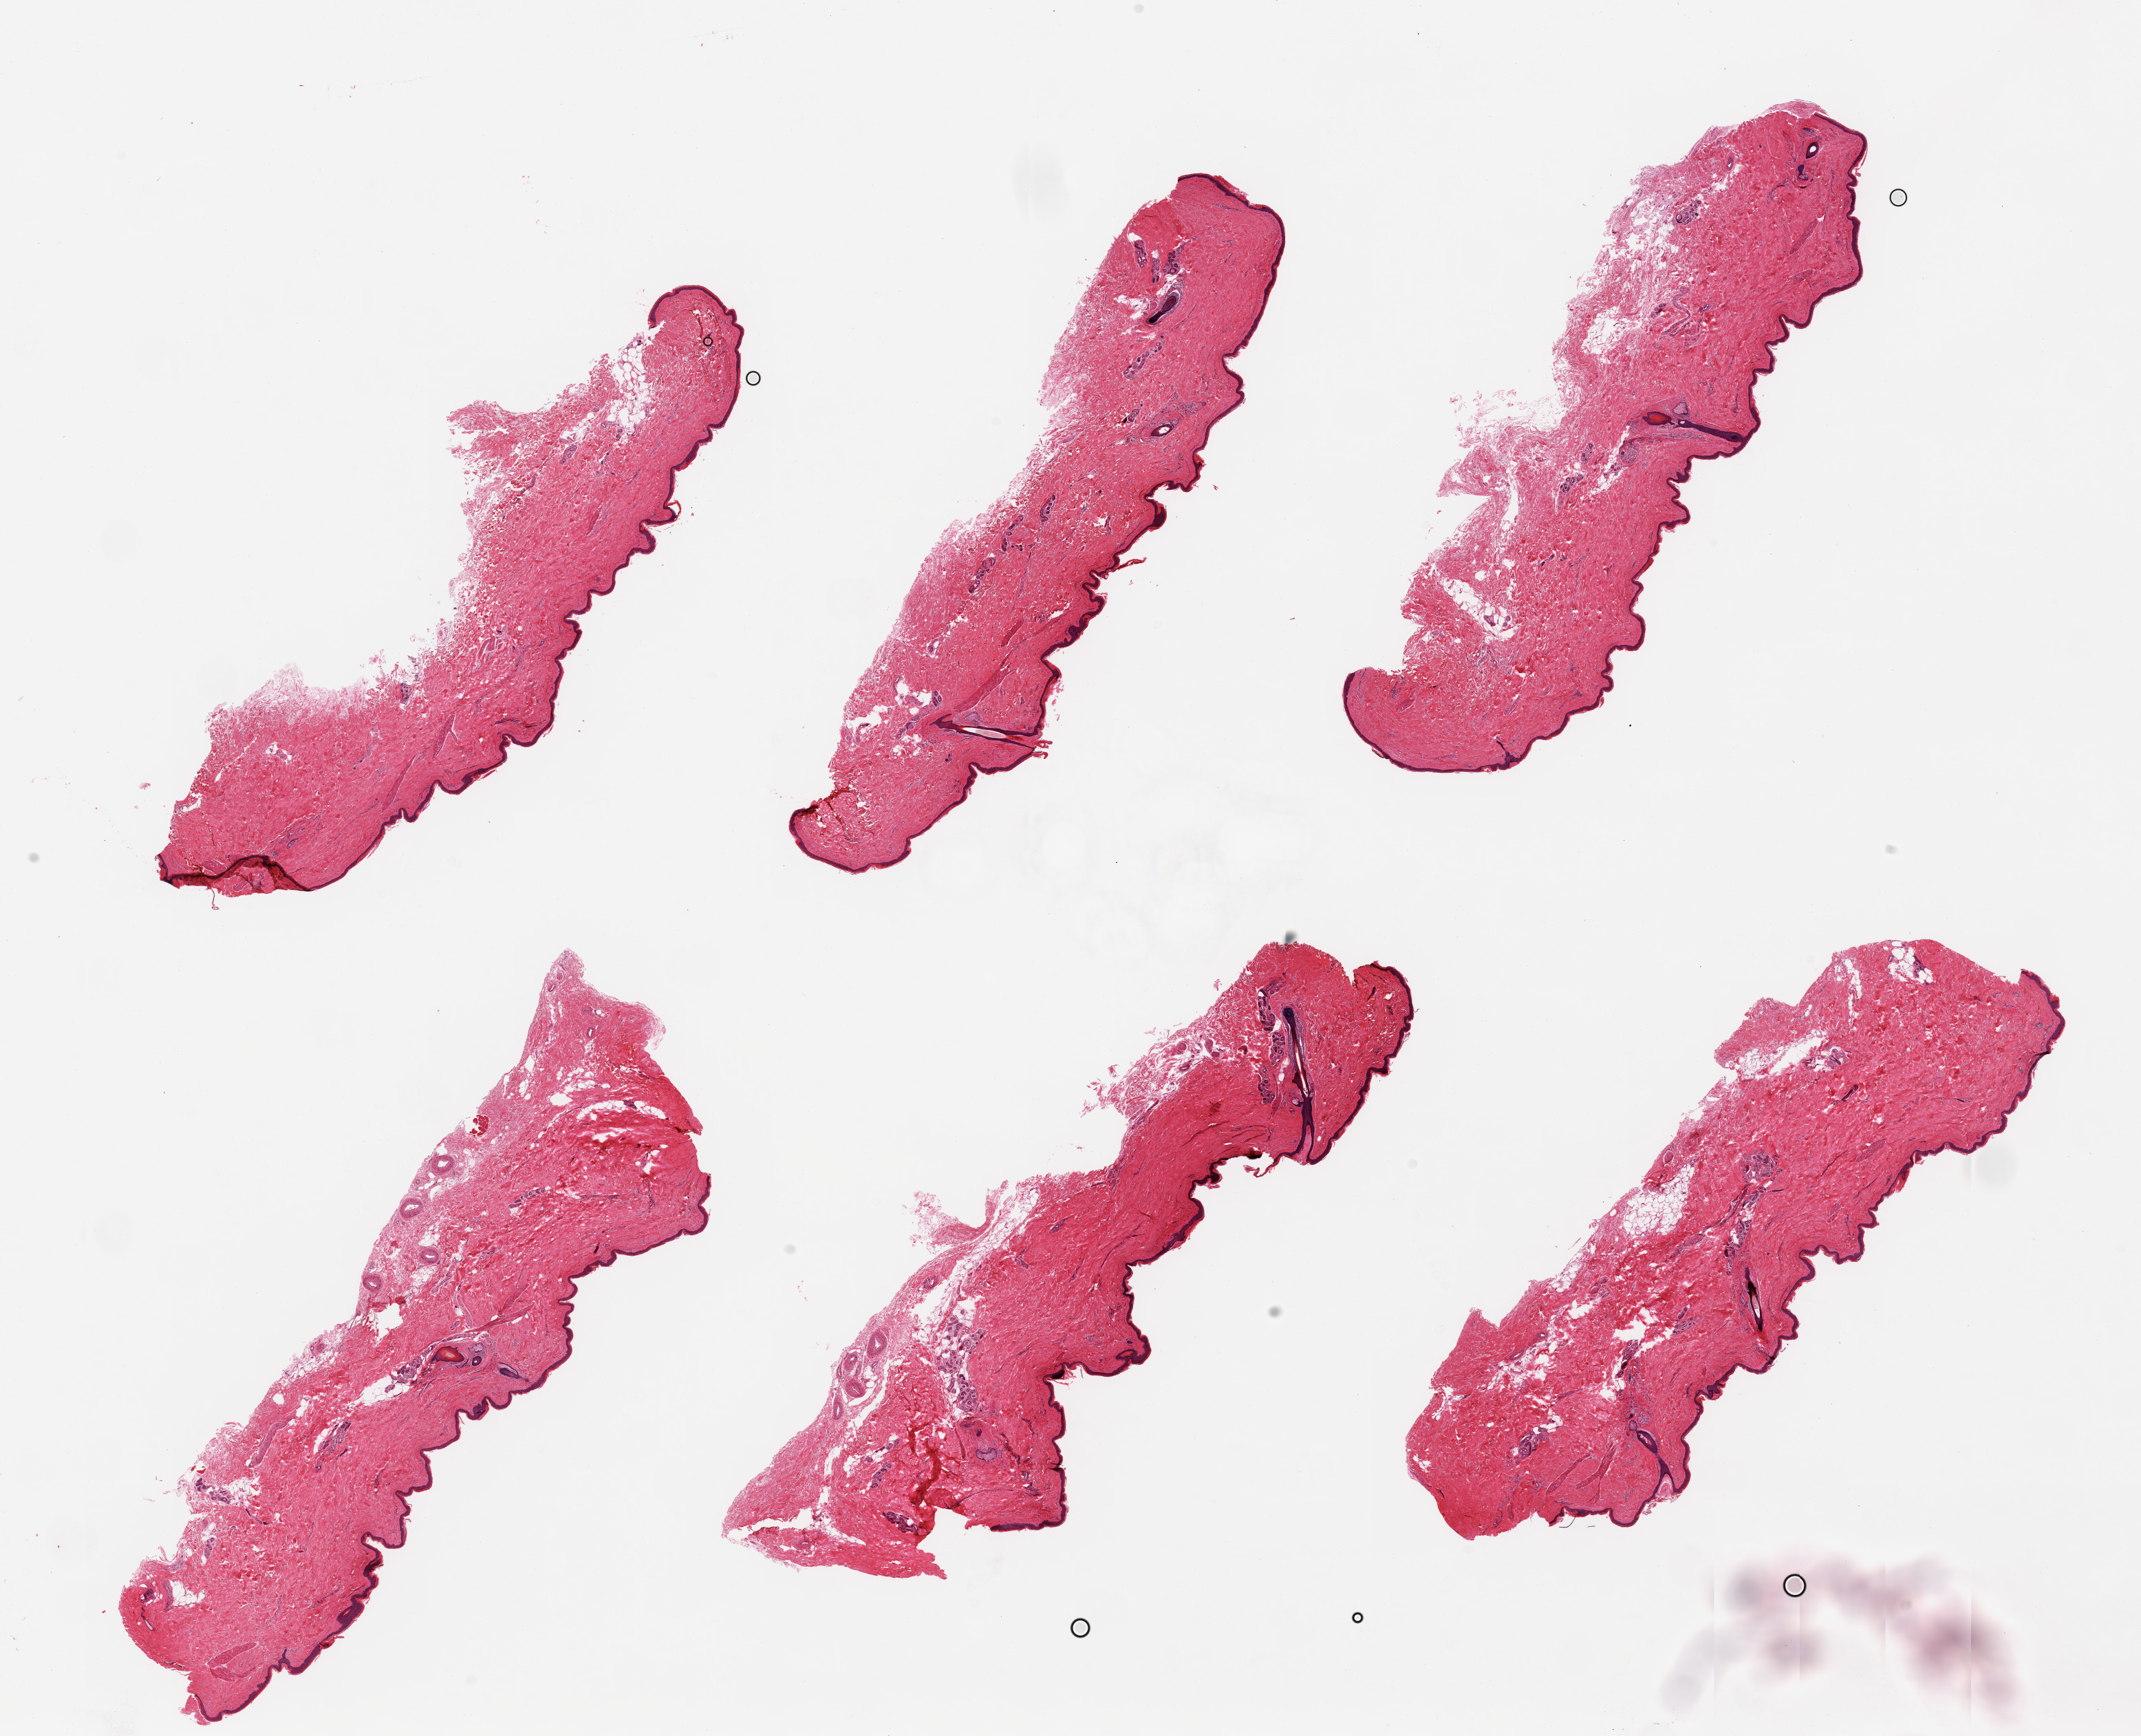
Digitized H&E-stained section, whole scanned area (about 24.6 x 20.0 mm, acquisition: 20x scan) shown as a low-resolution overview. PAXgene-fixed, paraffin-embedded tissue. Sampled site (target tissue): skin of lower leg. Donor tissue sample. Donor sex: male.
Review note (as recorded): 6 pieces, minimal dermal fat; squamous epithelium is ~40-45 microns.